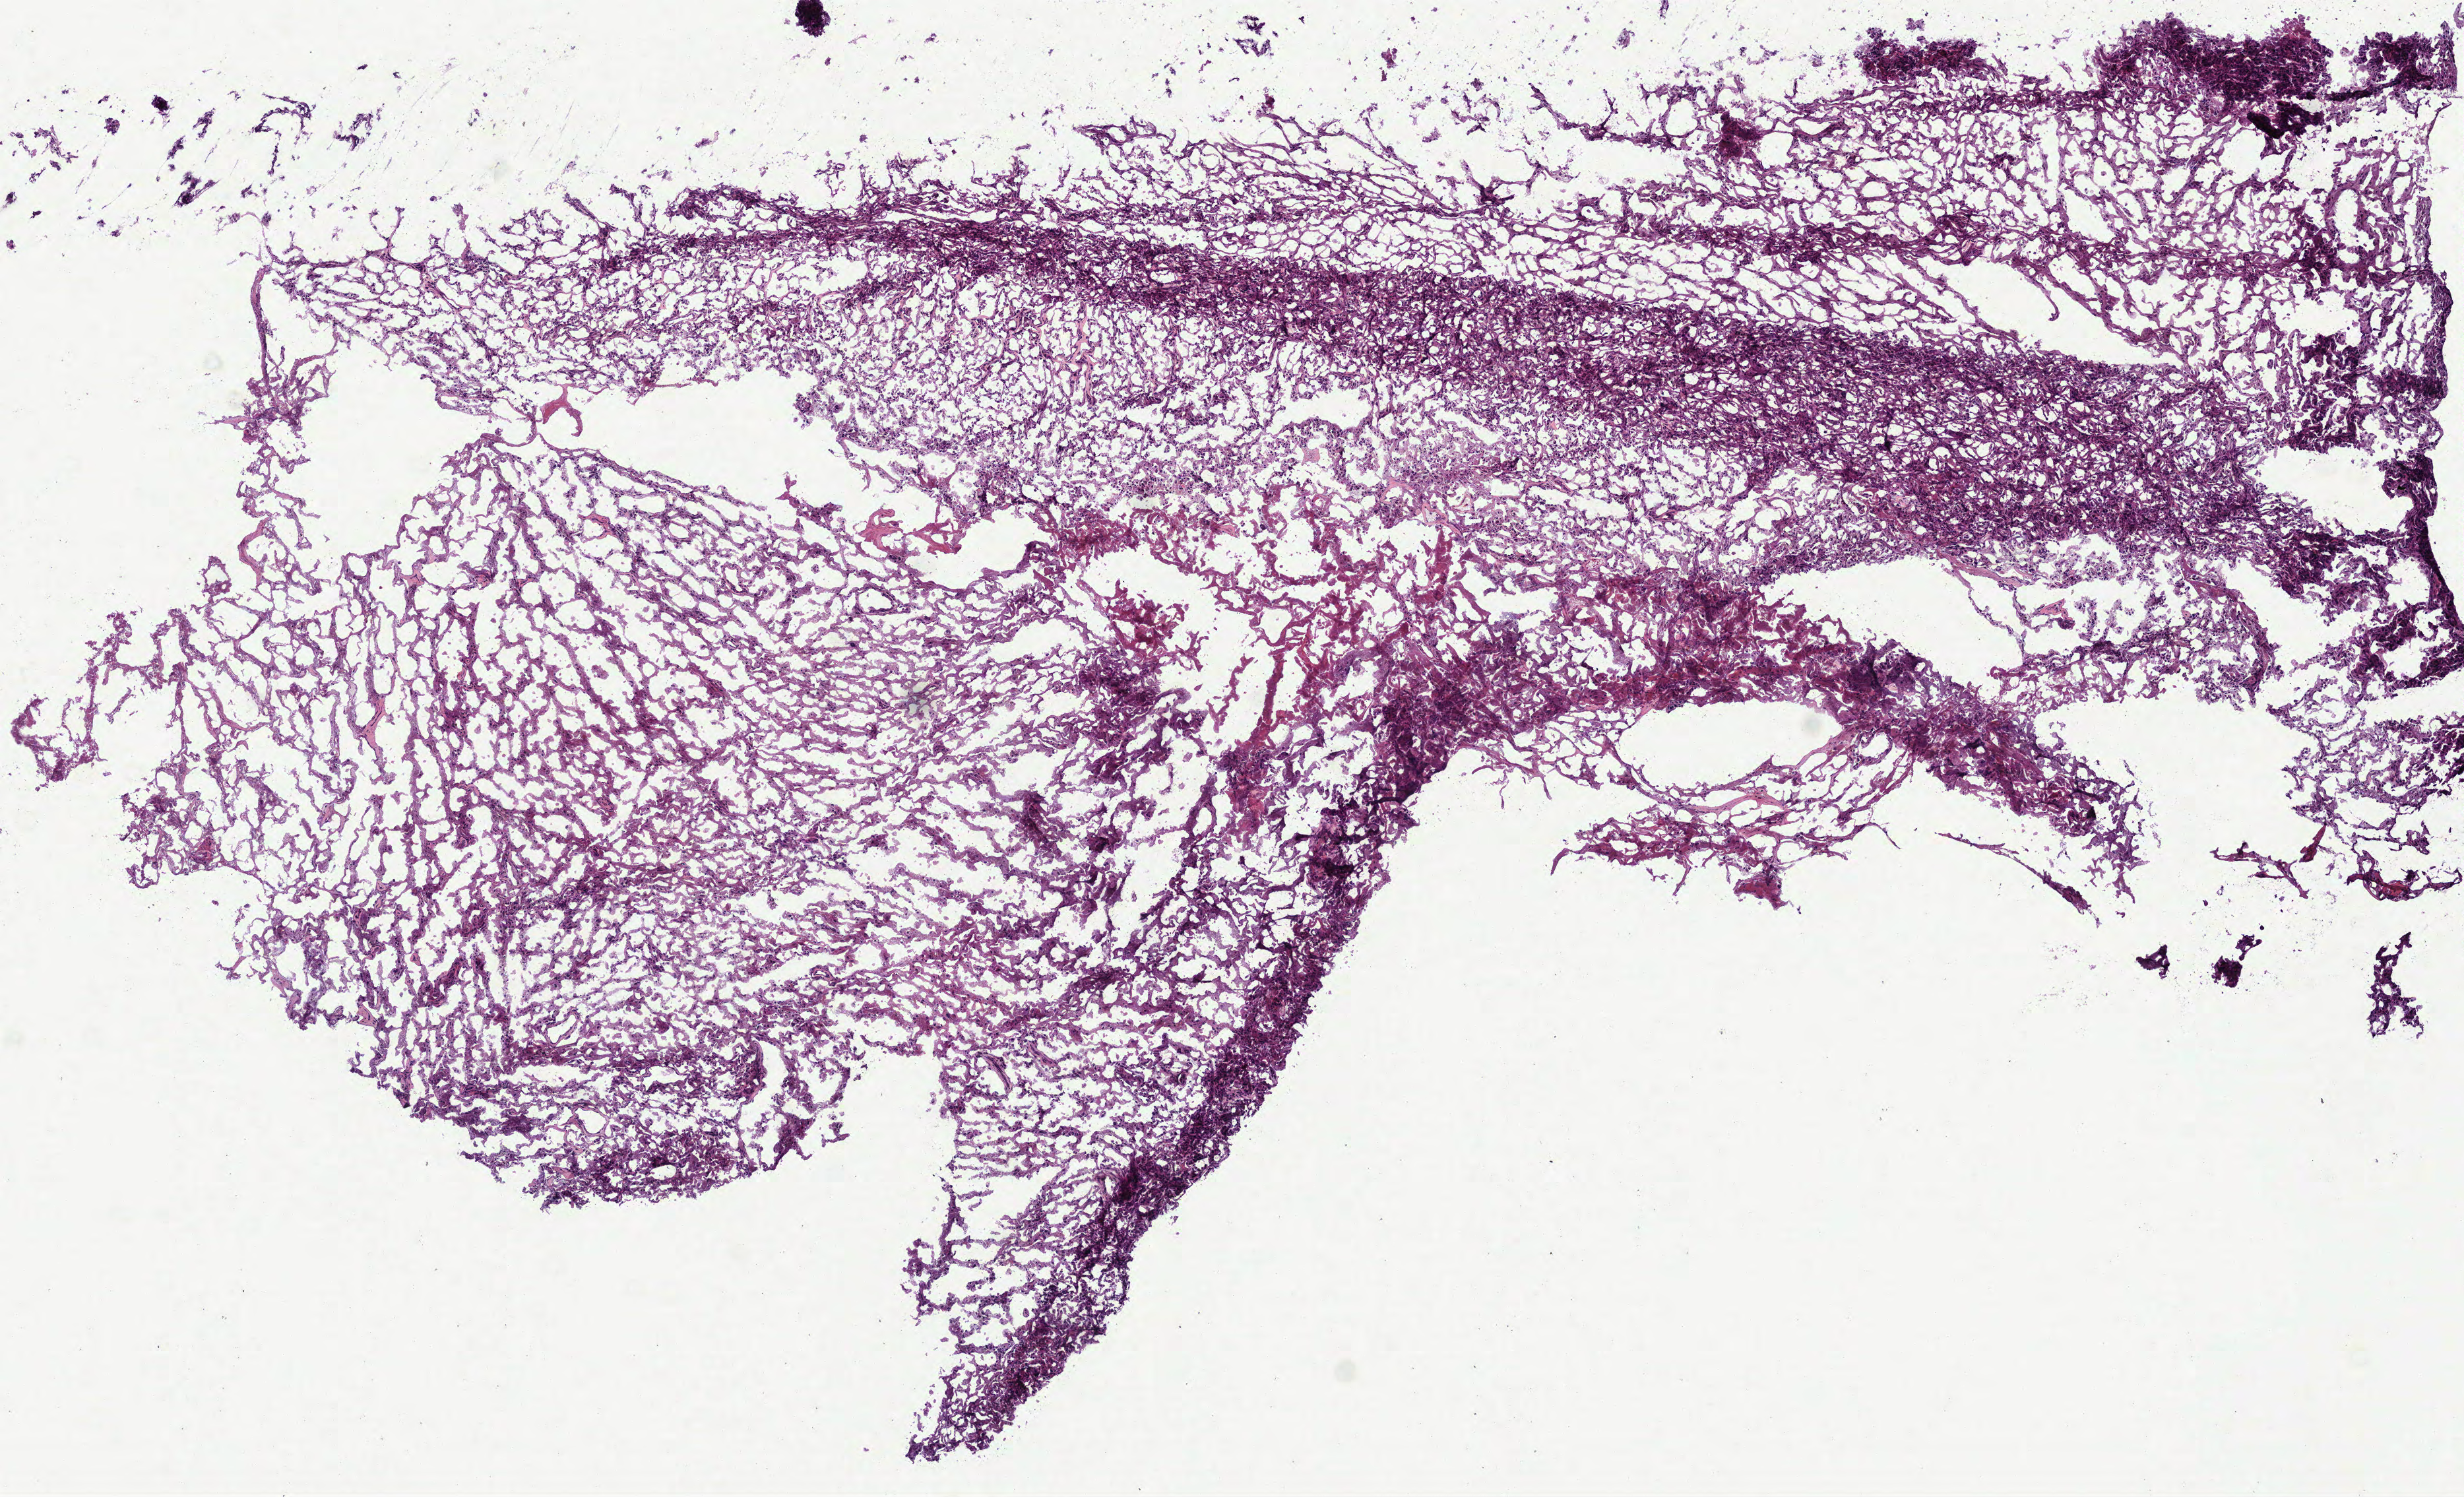
H&E-stained whole-slide image — low-resolution overview of the scanned area, about 7.5 x 4.6 mm (slide scanned at 40x), frozen section, brain, primary tumour sample. Patient: male, age at initial diagnosis 74 years.
Diagnosis: Glioblastoma.